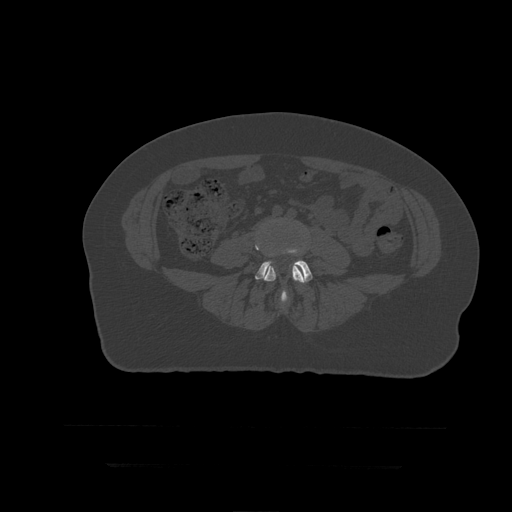
CT including the spine, one axial slice. Position 85 of 399 along the scan axis. 120 kVp. Bone window (W 1800 / L 400 HU). 512 × 512 image matrix, field of view 450 × 450 mm. Patient age 41 years. Case-level facts recorded for this patient, not image findings: primary cancer: breast.
Annotated regions visible in this slice (semi-automatically segmented with operator editing):
- L4 vertebra: bounding box [x1, y1, x2, y2] px = [256, 218, 306, 302]
- L5 vertebra: [256, 249, 313, 305]